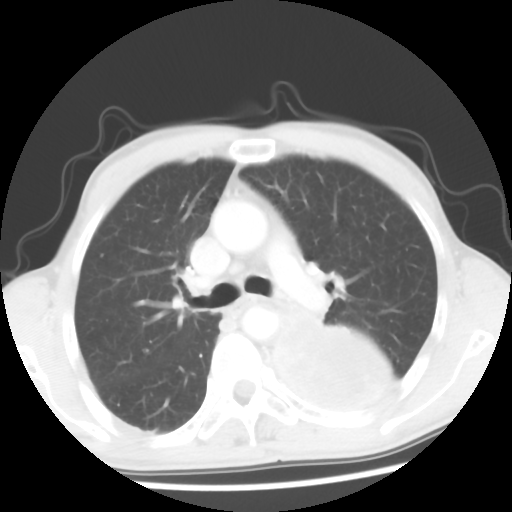
Chest CT, one axial slice; position 37 of 56 along the scan axis; 120 kVp; lung window (W 1500 / L -600 HU); 5 mm slice thickness; 512 × 512 image matrix. Male patient, age 60 years. Case-level facts recorded for this patient, not image findings: clinical TNM (as recorded): T4 N0 M0.
Outlined on this slice (rectangle marked by the reading radiologist):
- lung tumour (recorded histology: squamous cell carcinoma): bounding box [x1, y1, x2, y2] px = [257, 305, 422, 426]